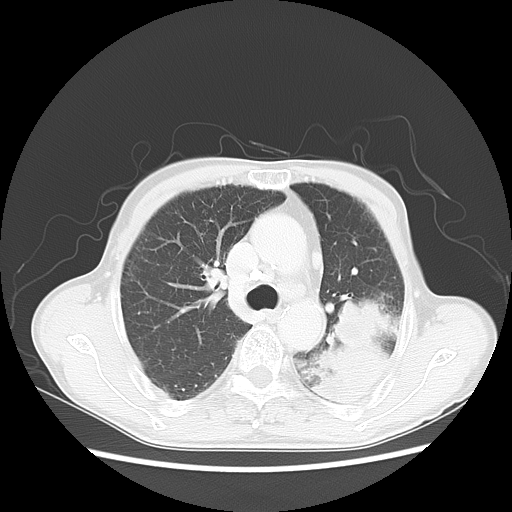
Chest CT, one axial slice. Position 36 of 51 along the scan axis. Reconstruction kernel LUNG. Lung window (W 1500 / L -600 HU). 5 mm slice thickness. 512 × 512 image matrix, field of view 360 × 360 mm. Patient: male, 64 years. From the clinical record (not read from this slice): clinical TNM (as recorded): T4 N0 M0; histopathological grade: G2-3.
Outlined on this slice (bounding box drawn by a radiologist):
- lung tumour (recorded histology: squamous cell carcinoma): bounding box (x1, y1, x2, y2) in pixels: (314, 283, 393, 409)